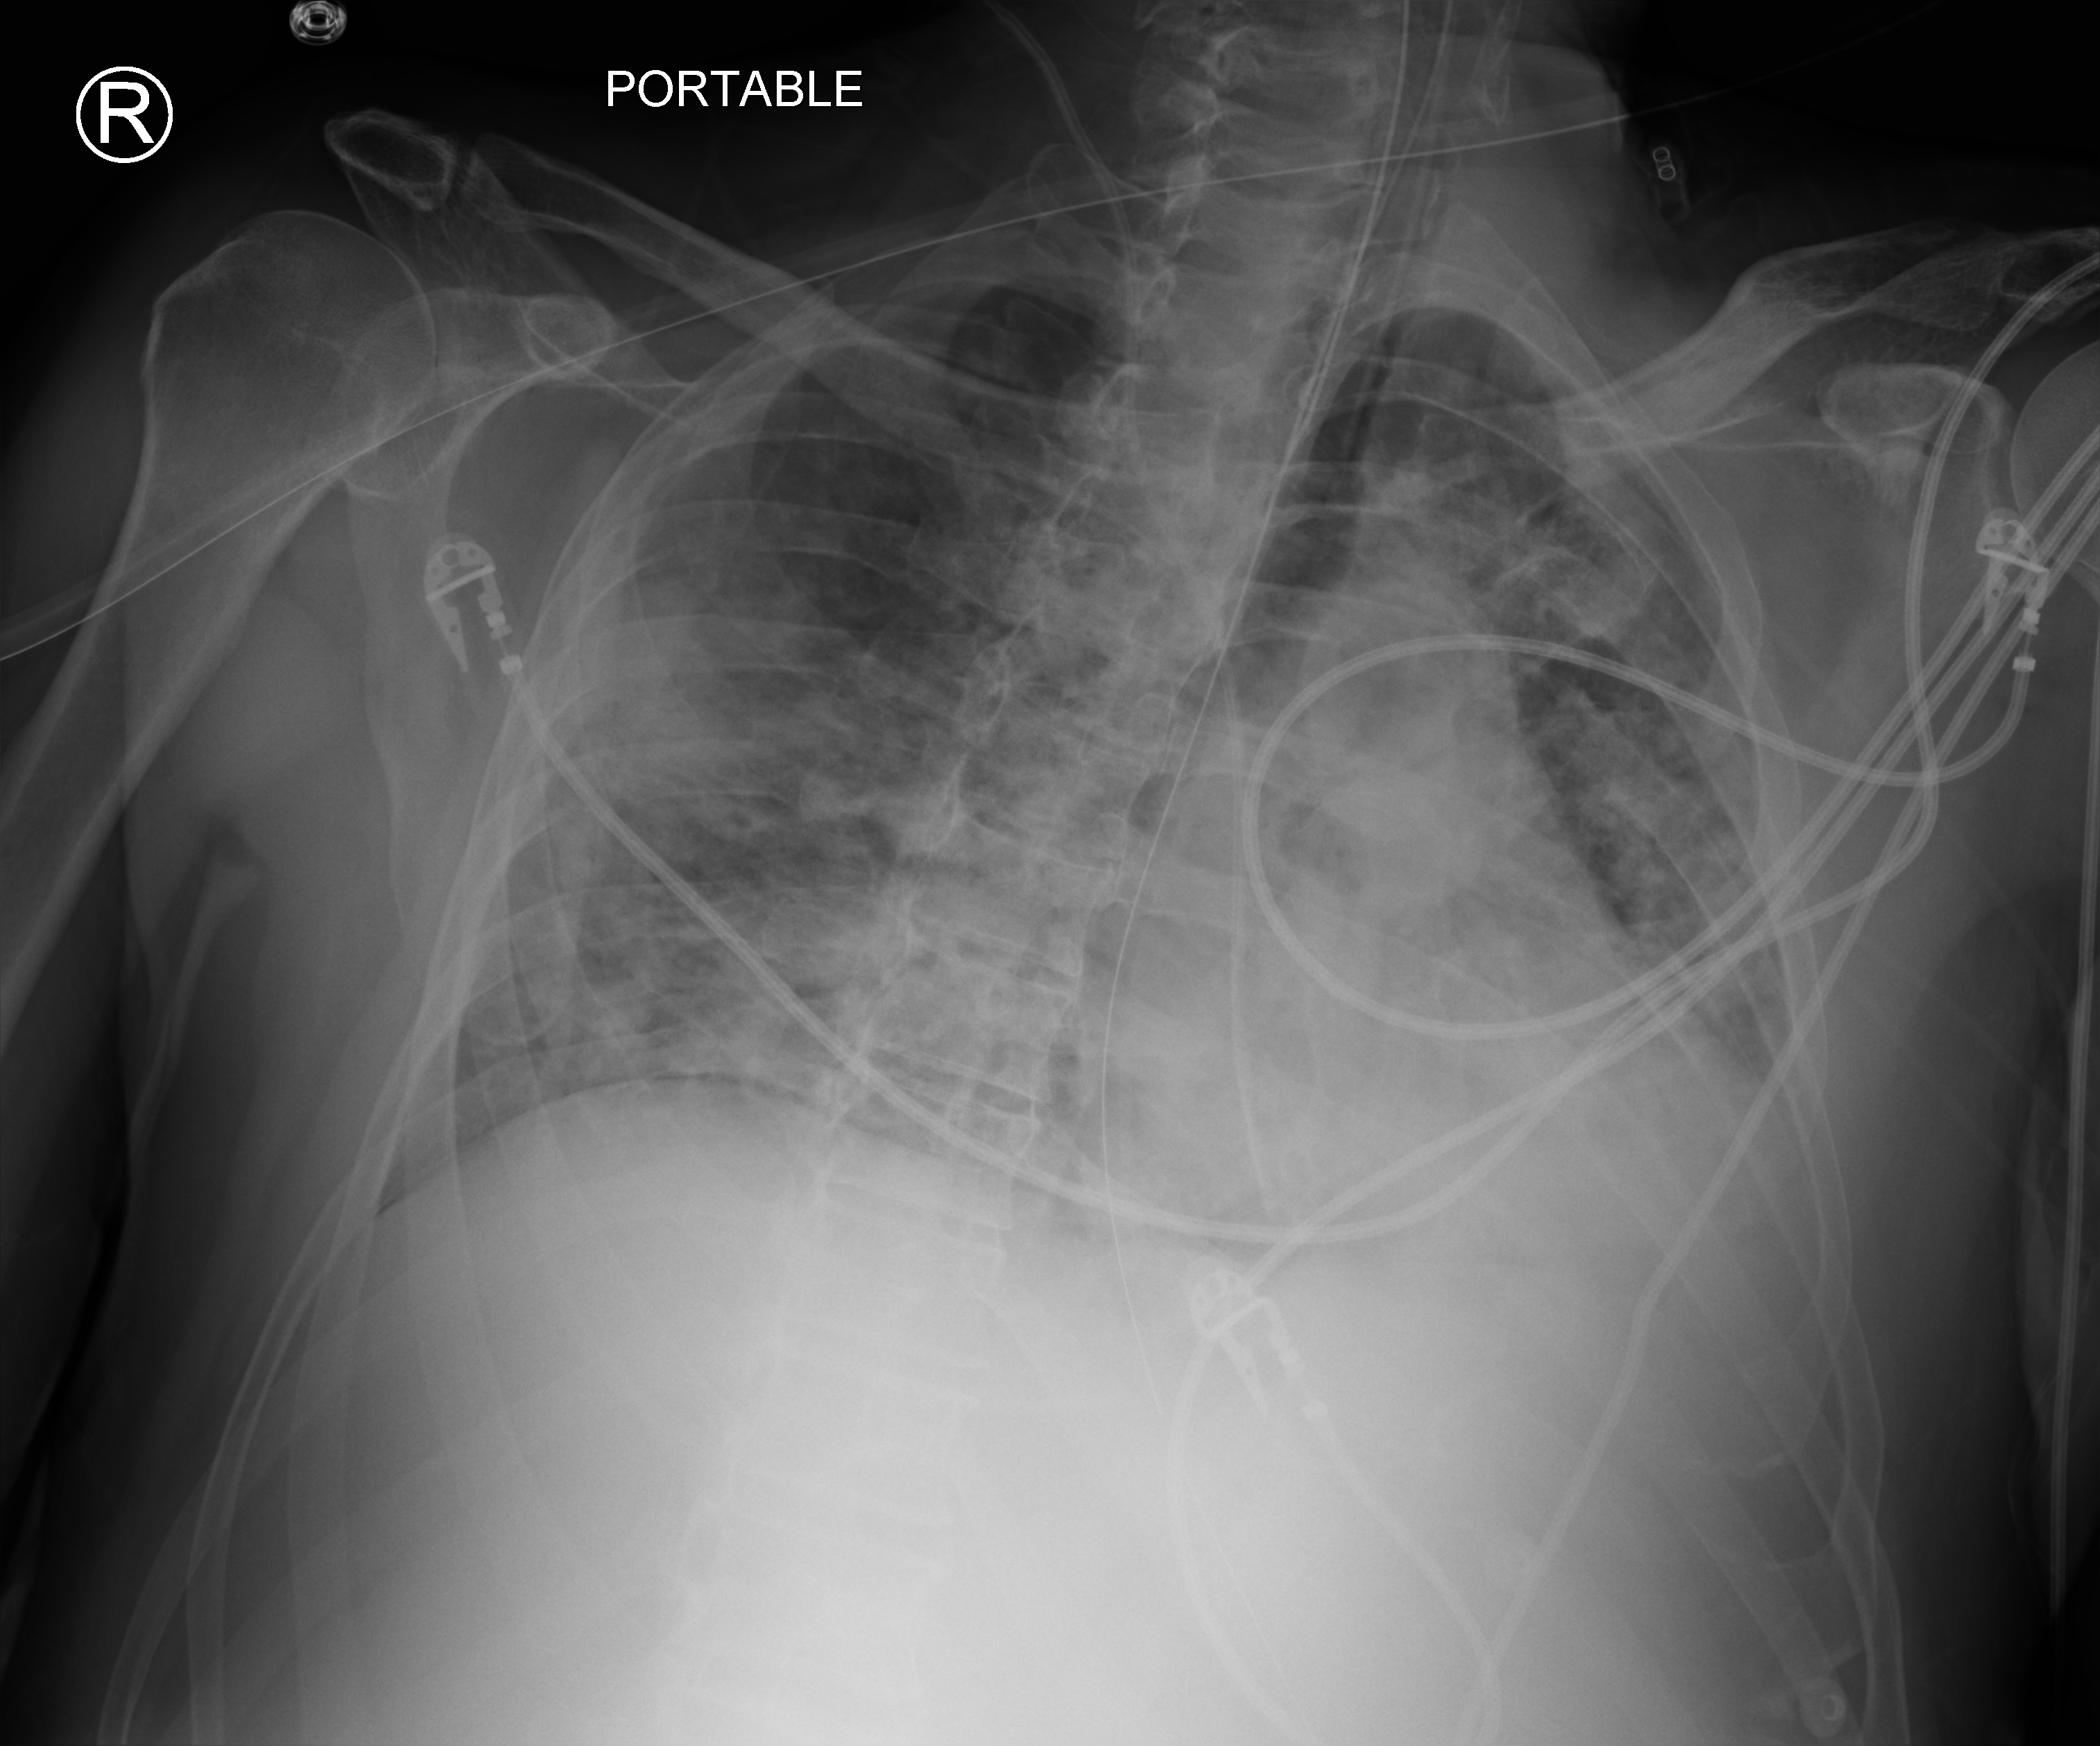
Portable chest radiograph; anteroposterior (AP) projection. Patient hospitalised with COVID-19; male, aged 18–59 years.
Admission-level facts for this patient (not findings on this image; timing relative to this image not recorded):
- length of hospital stay: 25 days